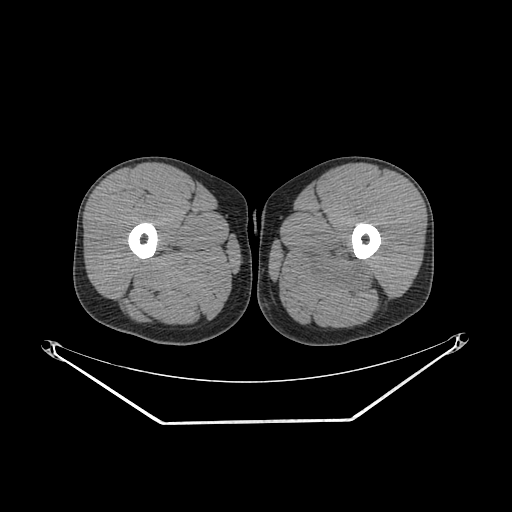
CT of an extremity soft-tissue mass (from a PET/CT study), one axial slice; position 243 of 267 along the scan axis; reconstruction kernel SOFT; 140 kVp; soft-tissue window (W 400 / L 40 HU); 512 × 512 image matrix. Male patient. Case-level facts recorded for this patient, not image findings: histological type: extraskeletal osteosarcoma; grade: high; site of the primary tumour: left adductur.
Structures marked on this image (expert contour drawn on MRI and transferred to this co-registered scan by the dataset authors):
- gross tumour volume (mass): bounding box (x1, y1, x2, y2) in pixels: (285, 240, 378, 298)